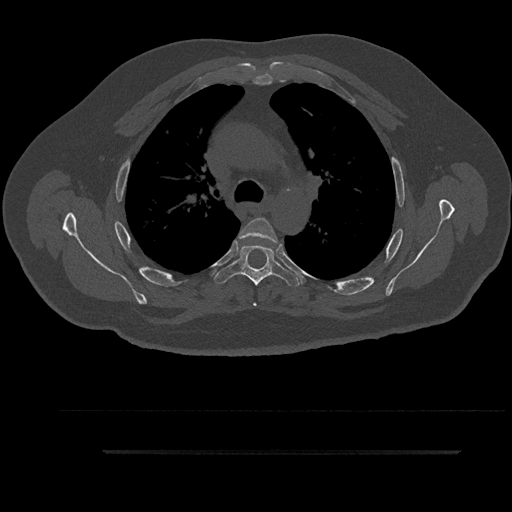
CT including the spine, one axial slice; slice 642 of 797 in the series (ordered by position); 120 kVp; bone window (W 1800 / L 400 HU); 512 × 512 image matrix, field of view 432 × 432 mm. Male patient, age 63 years. From the clinical record (not read from this slice): primary cancer: renal; vertebrae with lytic lesions (as recorded): T8.
Outlined on this slice (semi-automatically segmented with operator editing):
- T3 vertebra: box from (x=245, y=256) to (x=247, y=259) px
- T4 vertebra: (x=238, y=218)–(x=280, y=306)
- T5 vertebra: (x=215, y=245)–(x=299, y=289)